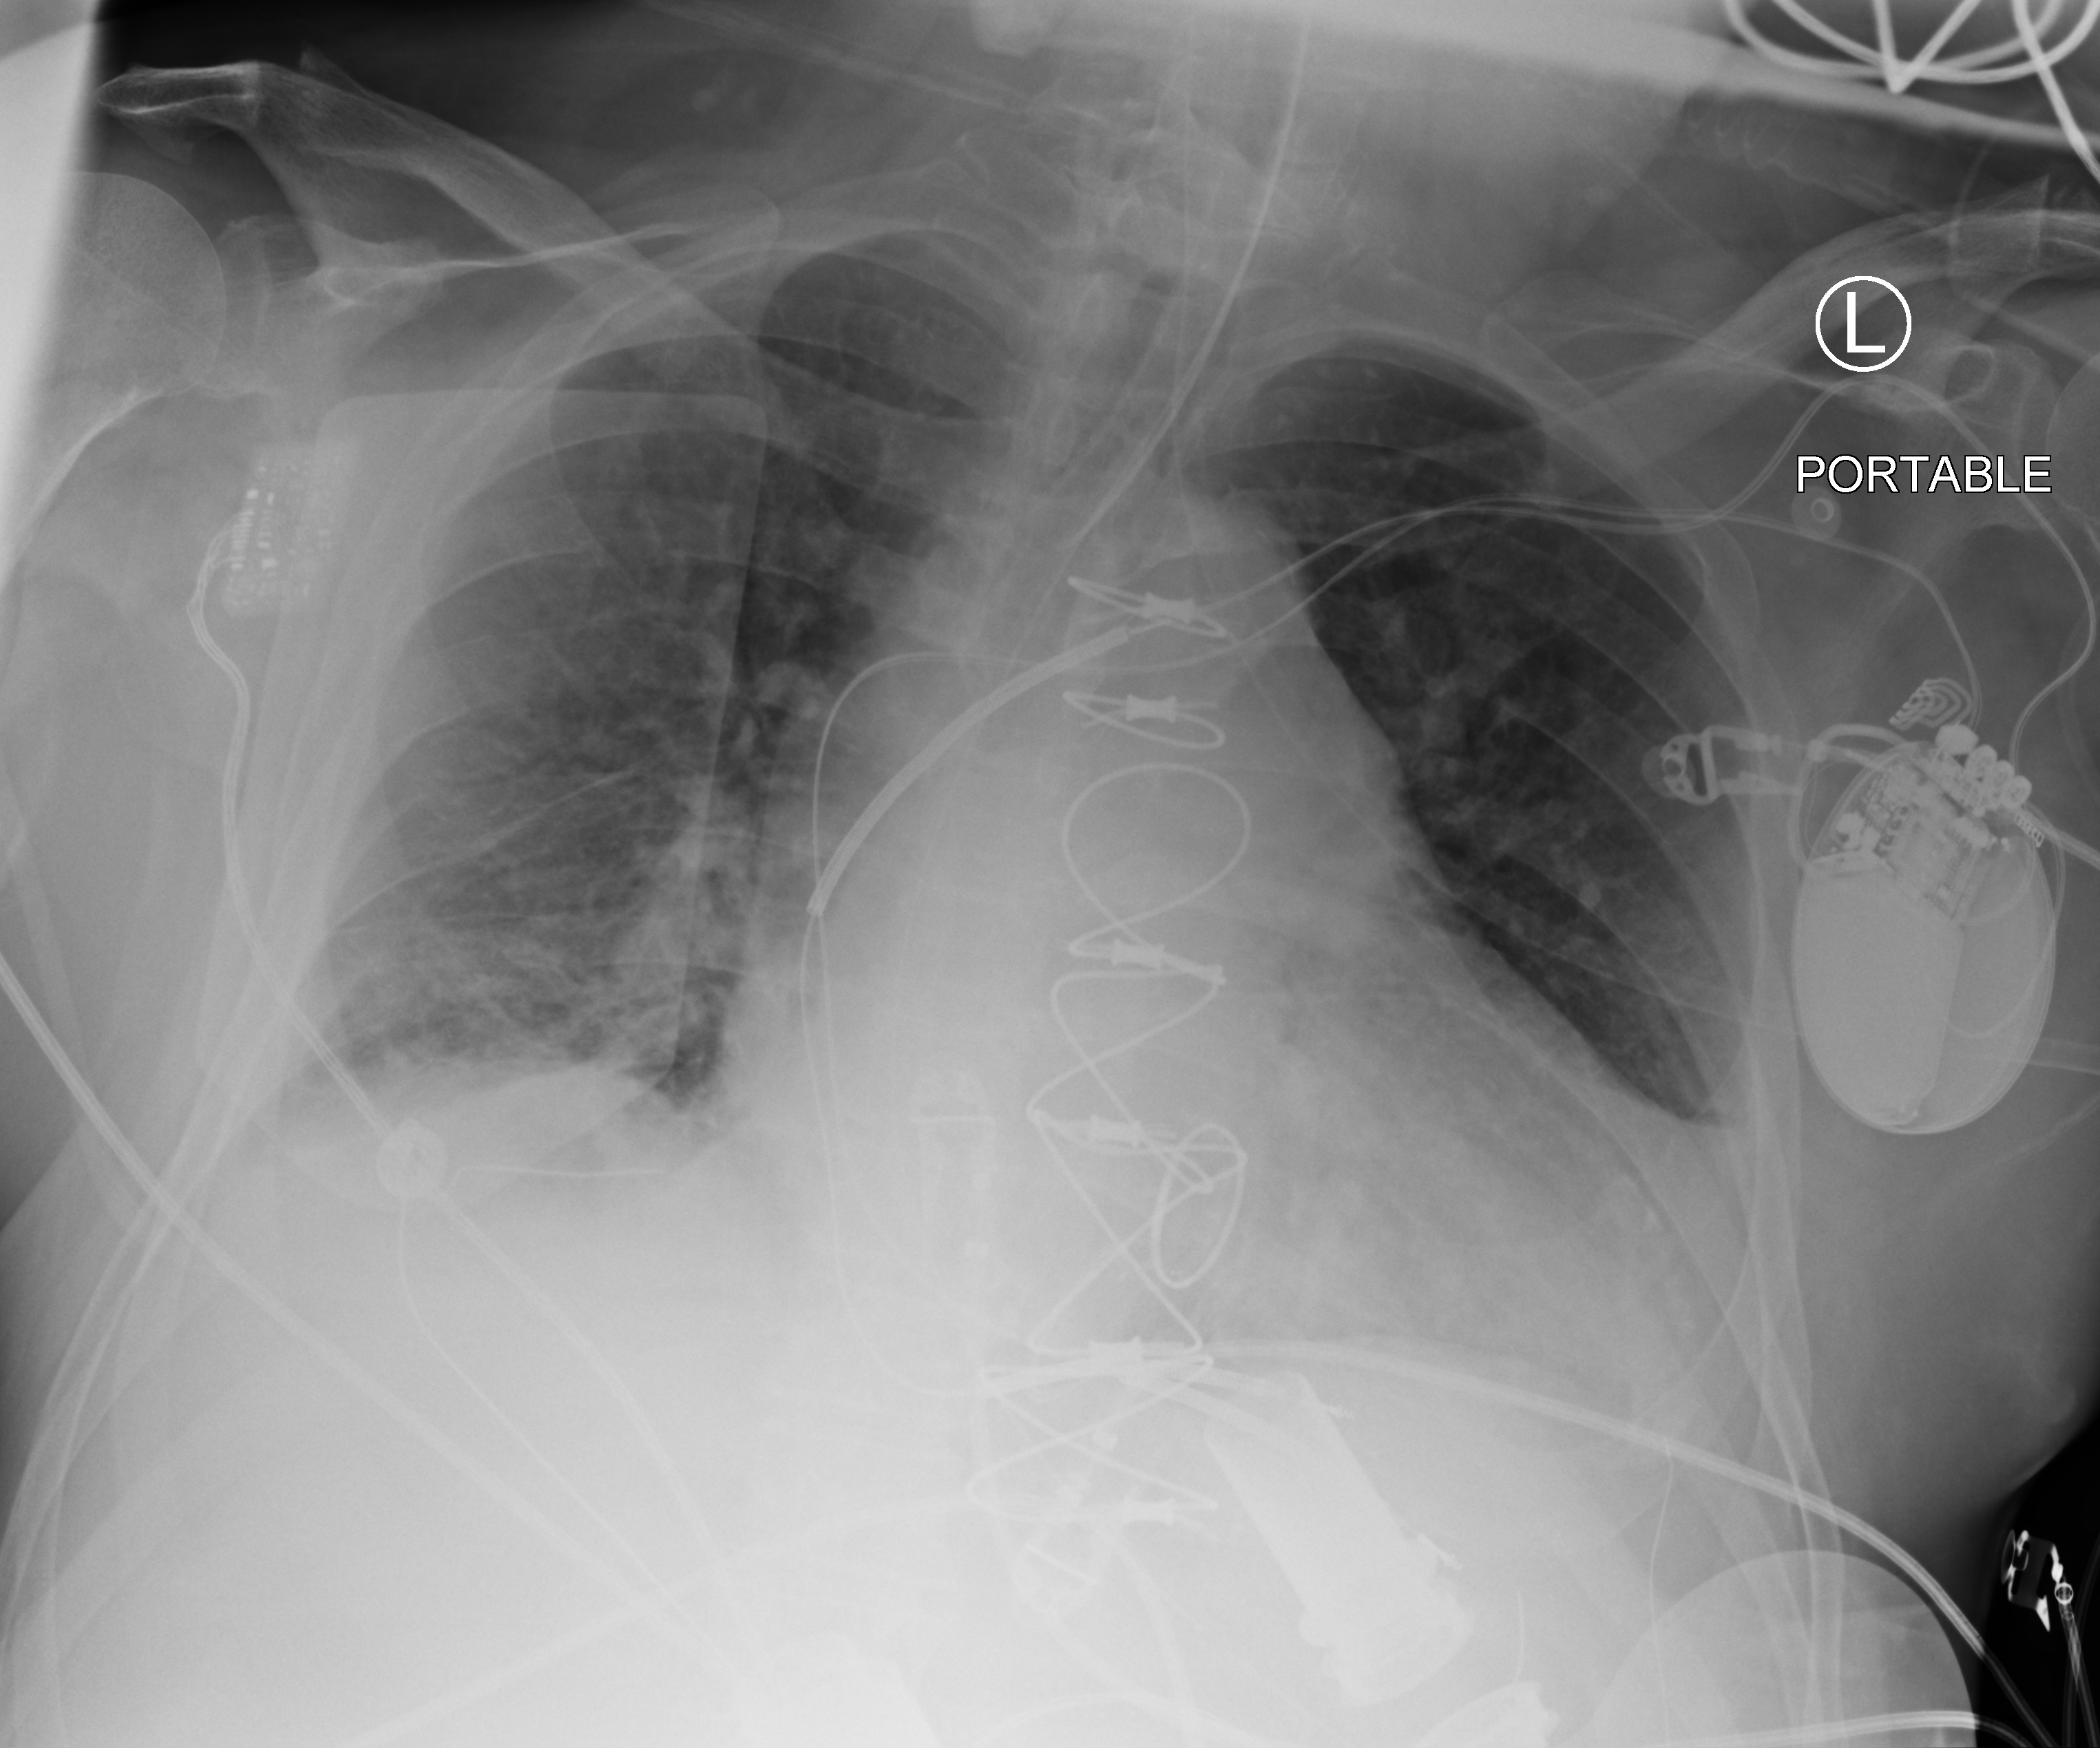
Chest X-ray (portable), anteroposterior (AP) projection. Patient hospitalised with COVID-19; male, aged 60–74 years.
From the hospital-stay record, not from the radiograph (when in the stay this image was taken is not recorded):
- admitted to intensive care during this hospital stay: yes